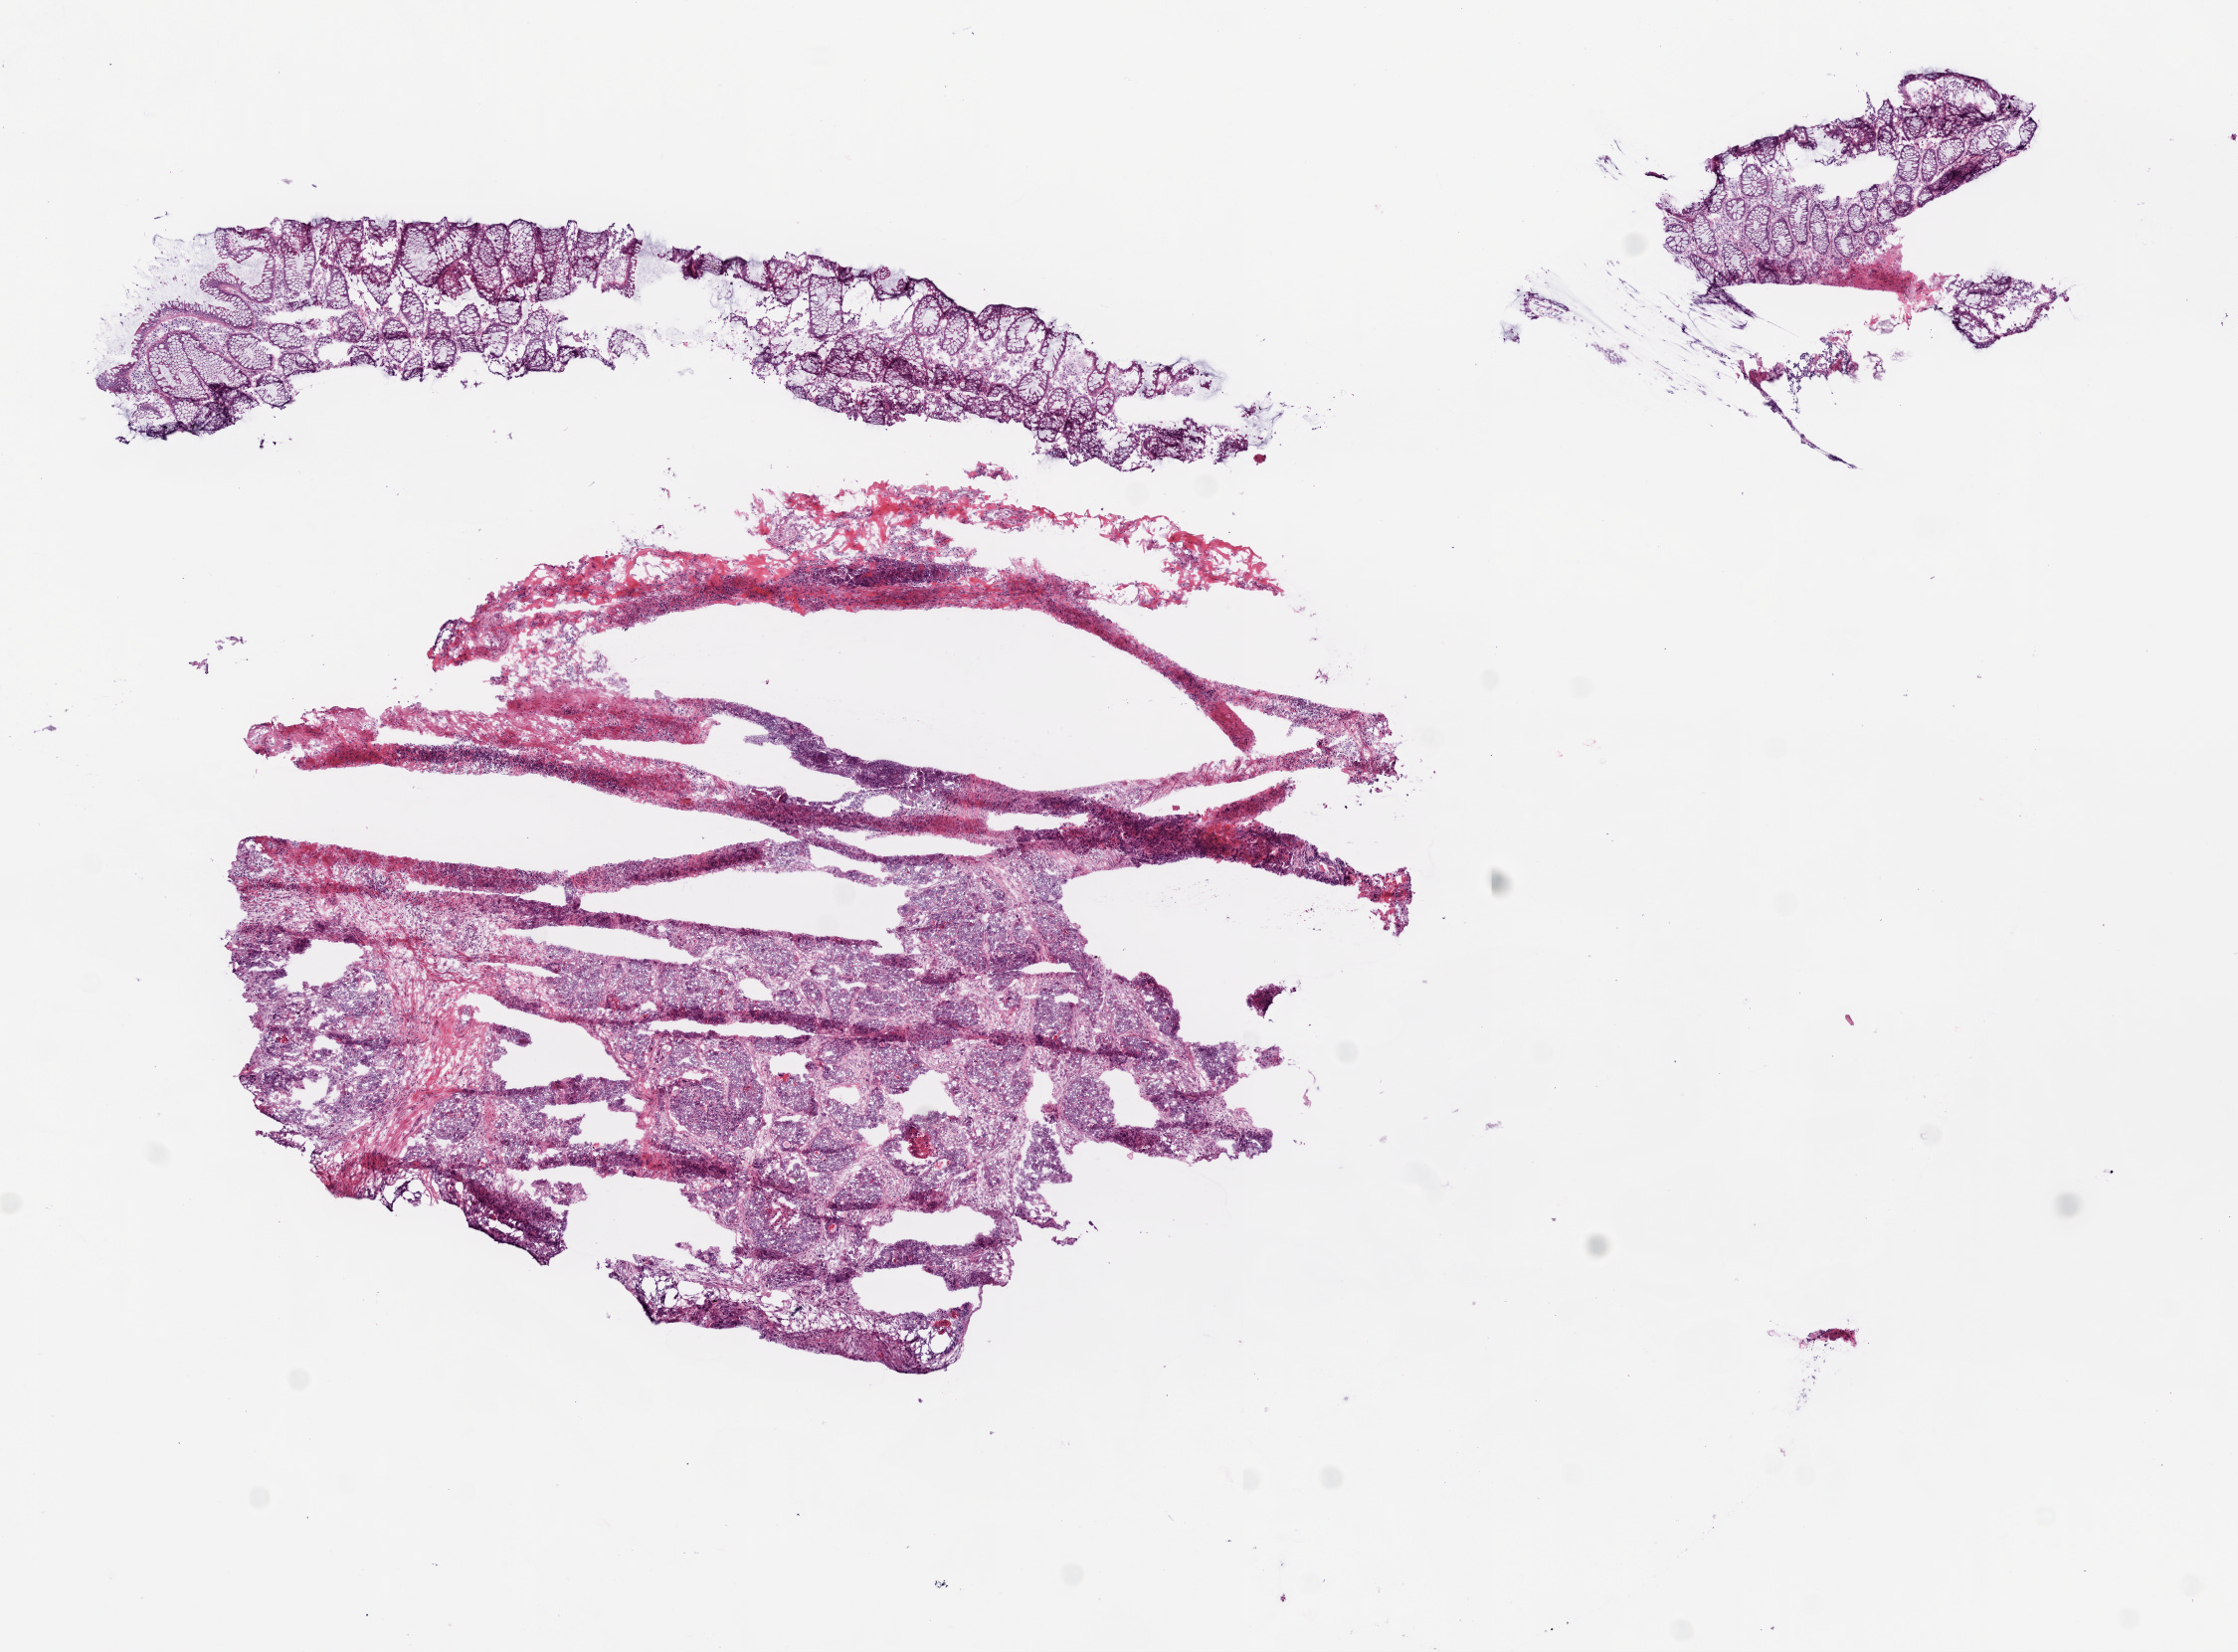
Digitized H&E-stained tissue section (whole slide), whole scanned area (about 9.0 x 6.7 mm, slide scanned at 20x) shown as a low-resolution overview. Frozen section from the bottom of the tissue portion. Colon, primary tumour sample. Female patient; age at initial diagnosis 54 years. Slide review estimates, as recorded: tumour cells 35%, tumour nuclei 60%, normal cells 20%, stromal cells 35%, necrosis 10%.
* AJCC pathologic stage: I
* diagnosis: Adenocarcinoma, NOS (sigmoid colon)